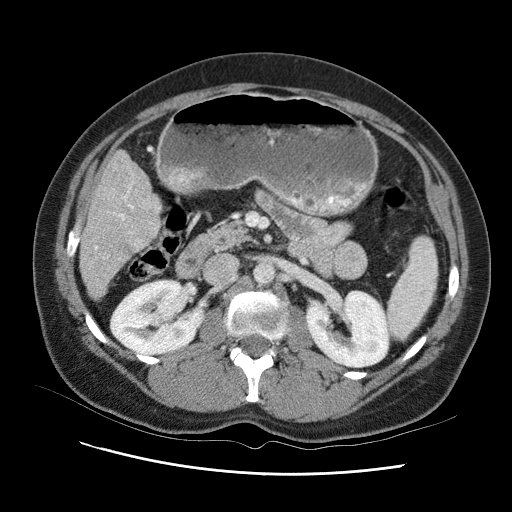
Contrast-enhanced abdominal CT (liver protocol), one axial slice. Position 35 of 95 along the scan axis. Reconstruction kernel STANDARD. 120 kVp. One of 2 acquisitions stored at this slice position. Soft-tissue window (W 400 / L 40 HU). 512 × 512 image matrix, field of view 360 × 360 mm. Case-level facts recorded for this patient, not image findings: diagnosis: hepatocellular carcinoma (patient treated with transarterial chemoembolisation; whether this scan precedes or follows treatment is not stated here); TNM stage (as recorded): Stage-I; Child-Pugh class: B; tumour differentiation: moderately differentiated.
Structures marked on this image (semi-automatically segmented with operator editing):
- liver parenchyma outside the tumour (the mass and vessels are separate outlines, so this box may not span the whole liver): bounding box [x1, y1, x2, y2] px = [80, 144, 168, 306]
- liver vessels: [100, 196, 142, 275]